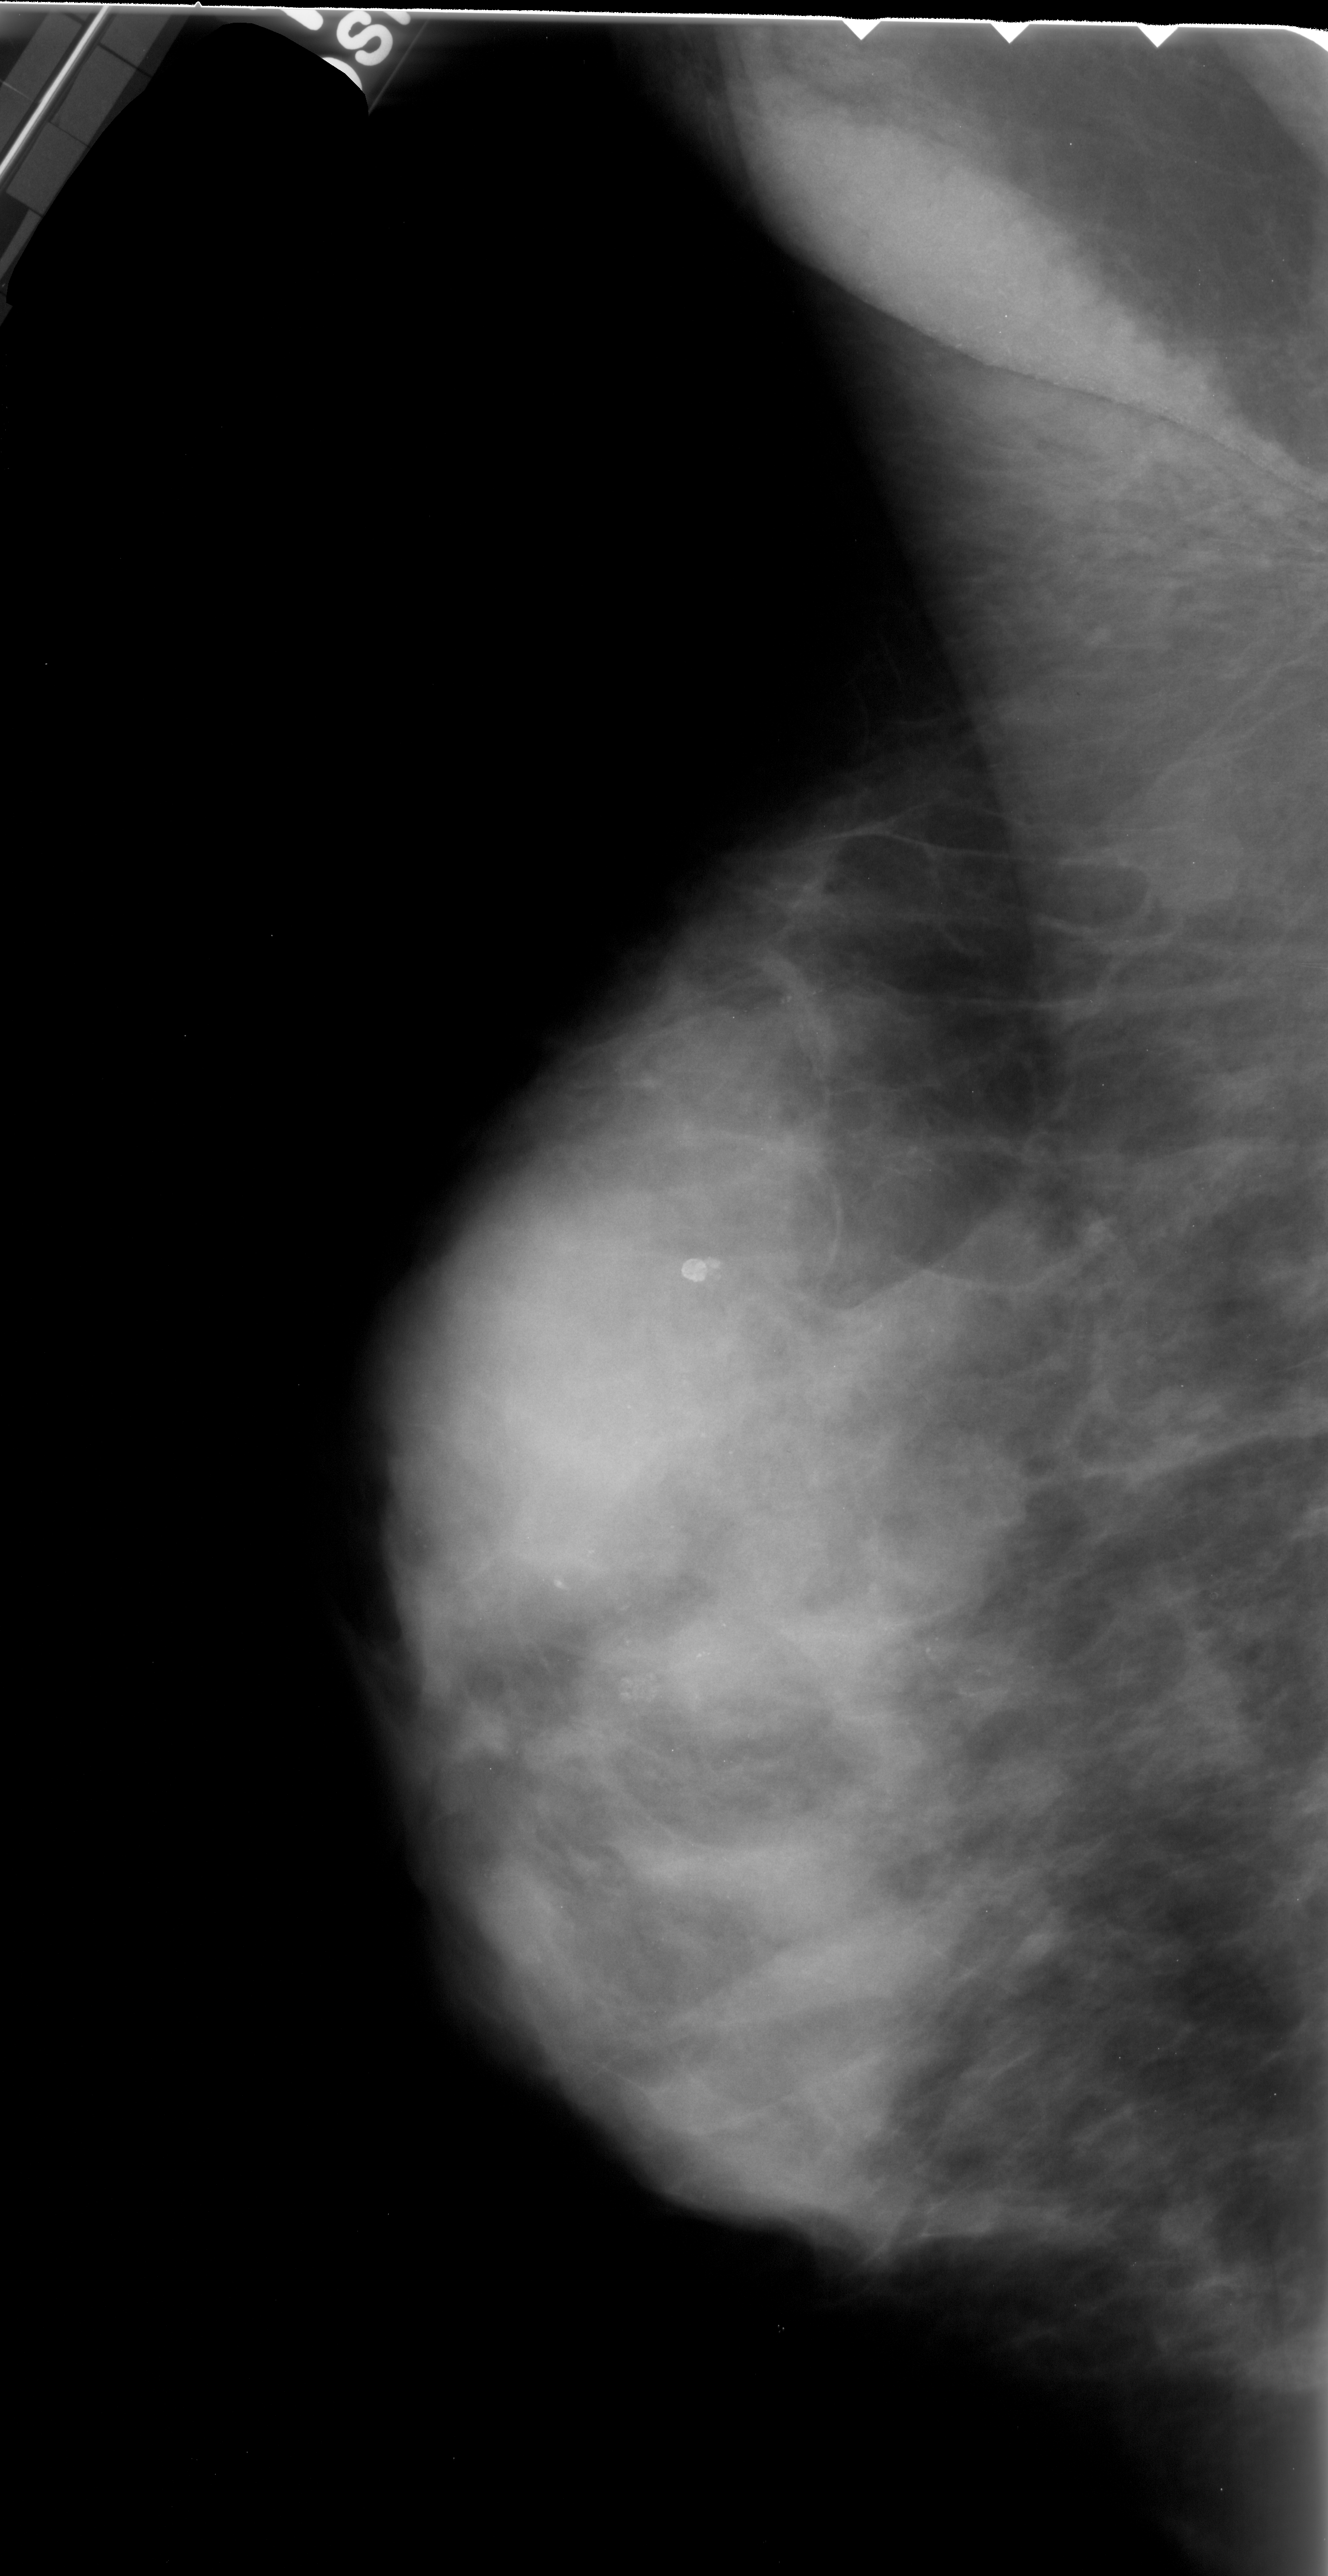
Mammogram (digitized film); left breast; MLO view; 1328 × 2576 image matrix.
Expert-marked regions of interest on this film, with their recorded descriptors:
- calcifications, morphology amorphous, distribution clustered; BI-RADS assessment category 4; subtlety rating 2 on a 1 (subtle) to 5 (obvious) scale; pathology result (as recorded, not read from the image): malignant: bounding box <600,1645,677,1719> (left, top, right, bottom; pixels)